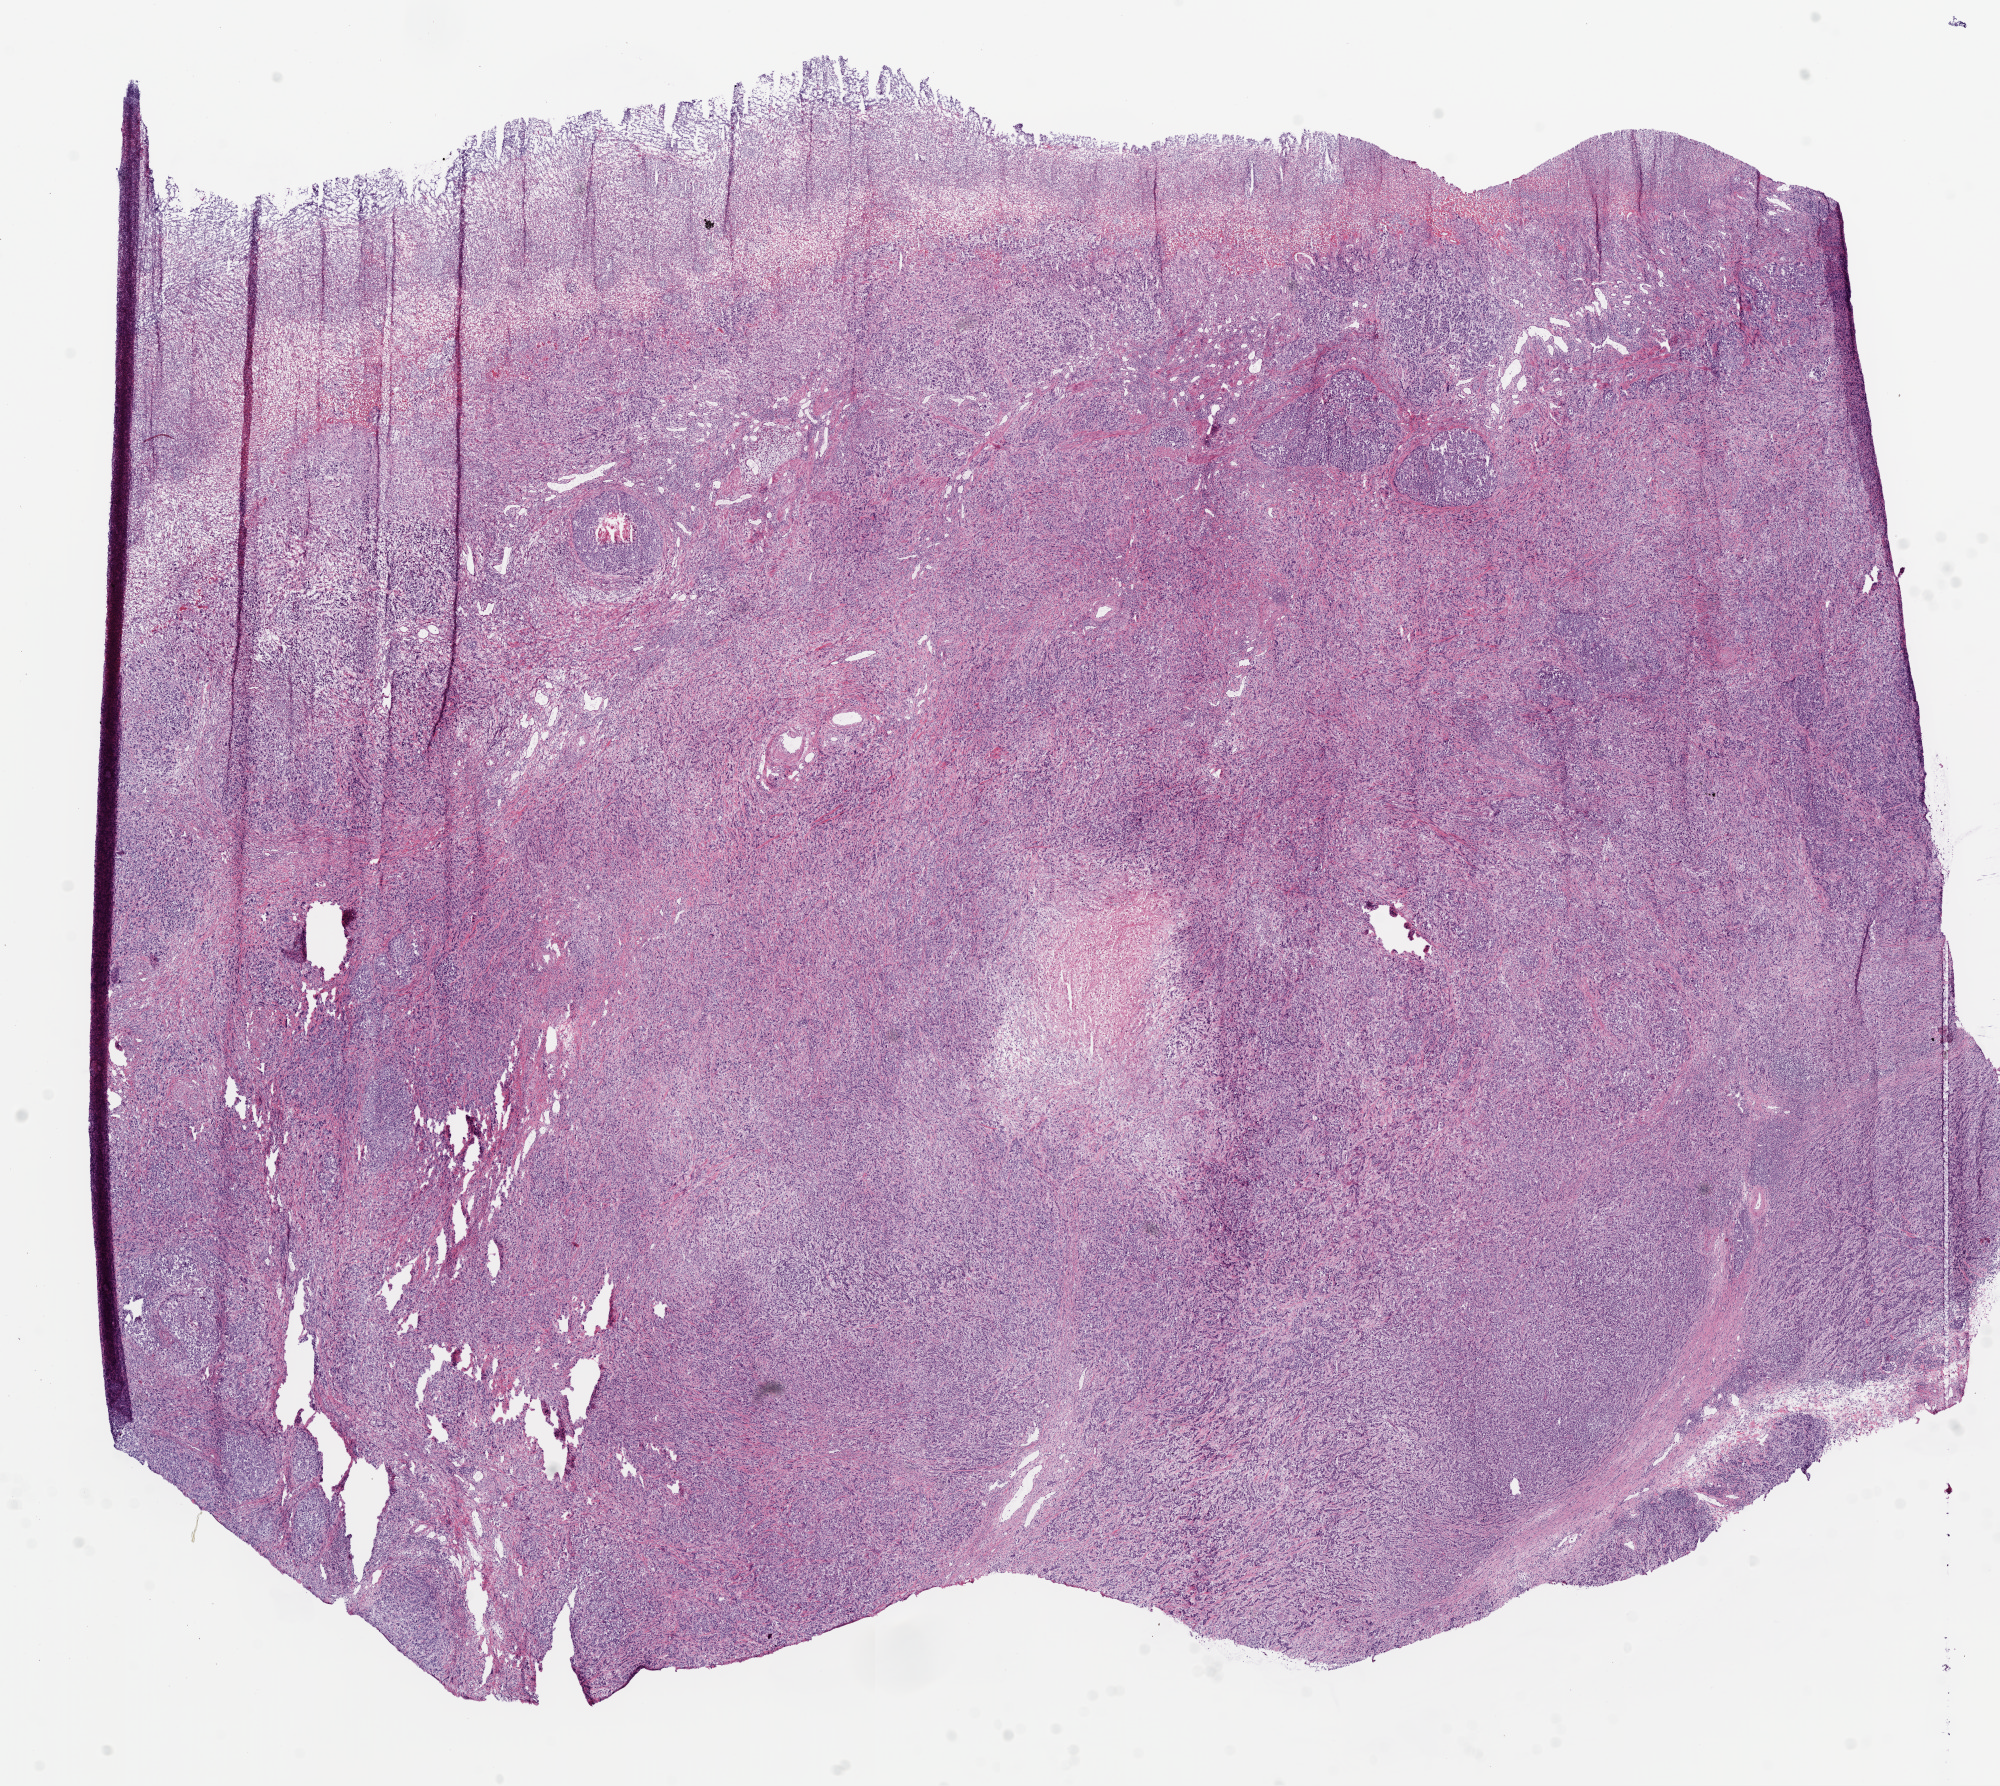
H&E whole-slide image — whole scanned area (about 16.0 x 14.3 mm) shown as a low-resolution overview. Frozen section. Sample: primary tumour, stomach. Patient: male, age at initial diagnosis 78 years. Histologic grade: G3 (poorly differentiated). Composition of this section per pathologist review: tumour cells 90%, tumour nuclei 75%, normal cells 0%, stromal cells 5%, necrosis 5%.
* lymph nodes positive (case pathology): 2 of 8 examined
* diagnosis: Adenocarcinoma, NOS